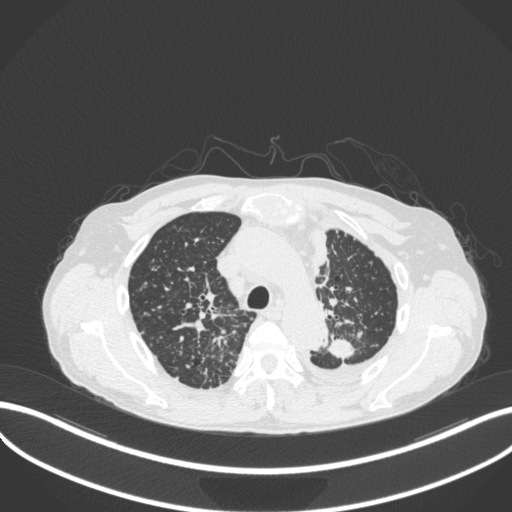
Chest CT, one axial slice. Position 263 of 319 along the scan axis. Lung window (W 1500 / L -600 HU). 1 mm slice thickness. 512 × 512 image matrix. Patient: male, 58 years. Case-level facts recorded for this patient, not image findings: clinical TNM (as recorded): T1c N3 M1.
Annotated regions visible in this slice (rectangle marked by the reading radiologist):
- lung tumour (recorded histology: adenocarcinoma): box from (x=322, y=334) to (x=365, y=364) px